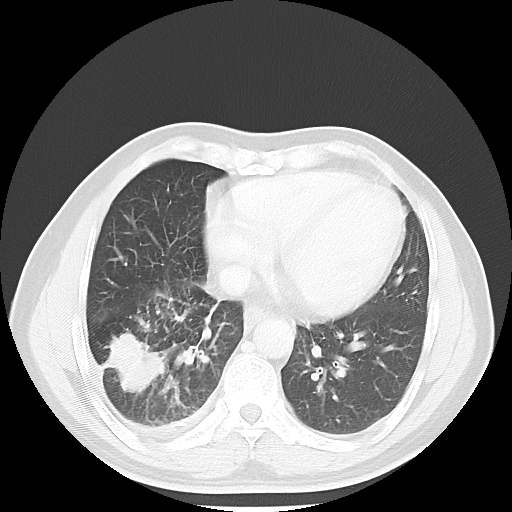
Chest CT, one axial slice; slice 20 of 56 in the series (ordered by position); reconstruction kernel LUNG; lung window (W 1500 / L -600 HU); 512 × 512 image matrix, field of view 344 × 344 mm. Patient: male, 56 years. Case-level facts recorded for this patient, not image findings: clinical TNM (as recorded): T2 N3 M1.
Outlined on this slice (bounding box drawn by a radiologist):
- lung tumour (recorded histology: adenocarcinoma): bounding box (x1, y1, x2, y2) in pixels: (104, 327, 172, 403)